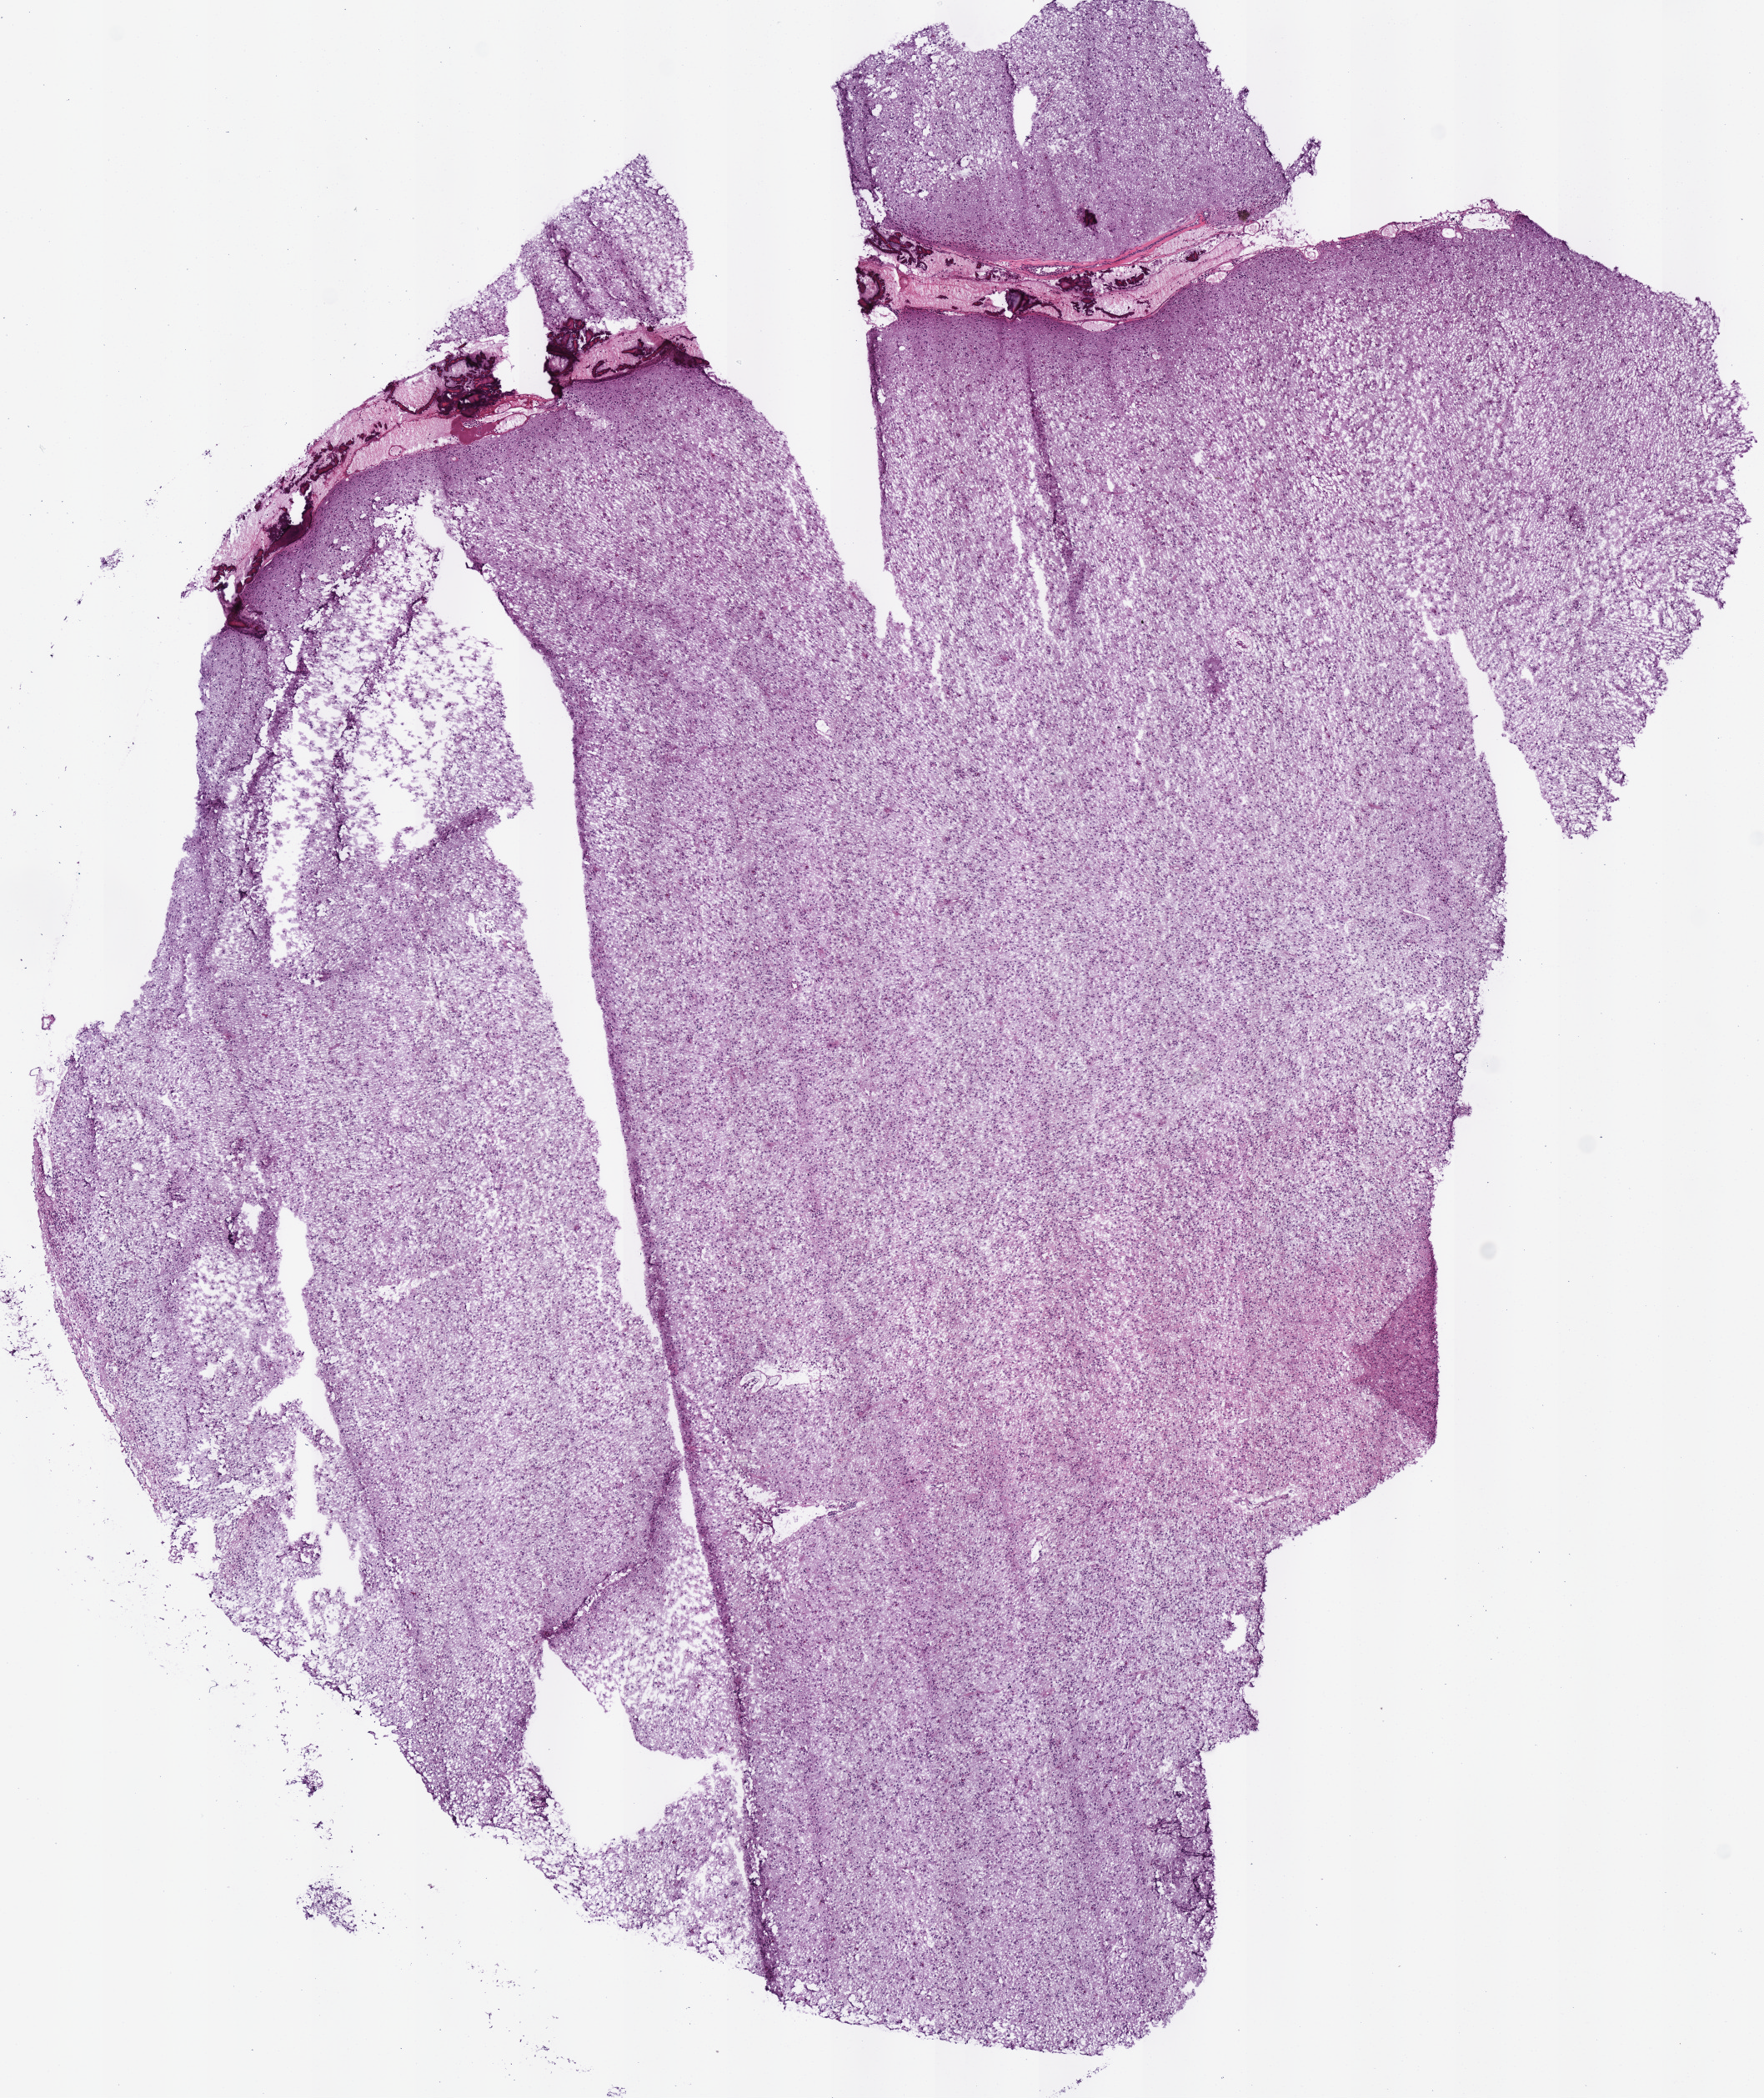
Digitized H&E tissue section (whole slide), whole scanned area (about 8.3 x 9.9 mm, slide scanned at 40x) shown as a low-resolution overview, frozen section from the bottom of the tissue portion, sample: primary tumour, brain. Patient: female, age at initial diagnosis 42 years.
Pathologic diagnosis: Mixed glioma (cerebrum).